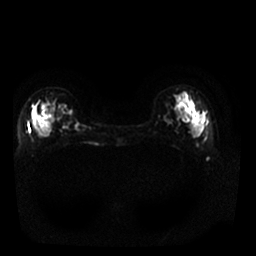
Breast MRI, one axial slice. Position 6 of 25 along the scan axis. Diffusion-weighted series; image 2 of 4 stored at this slice position (different b-values; order by instance number). 1.5 T. 256 × 256 image matrix. Female patient.
Outlined on this slice (manually delineated by an expert):
- tumour on diffusion-weighted imaging: bounding box (x1, y1, x2, y2) in pixels: (34, 110, 44, 136)